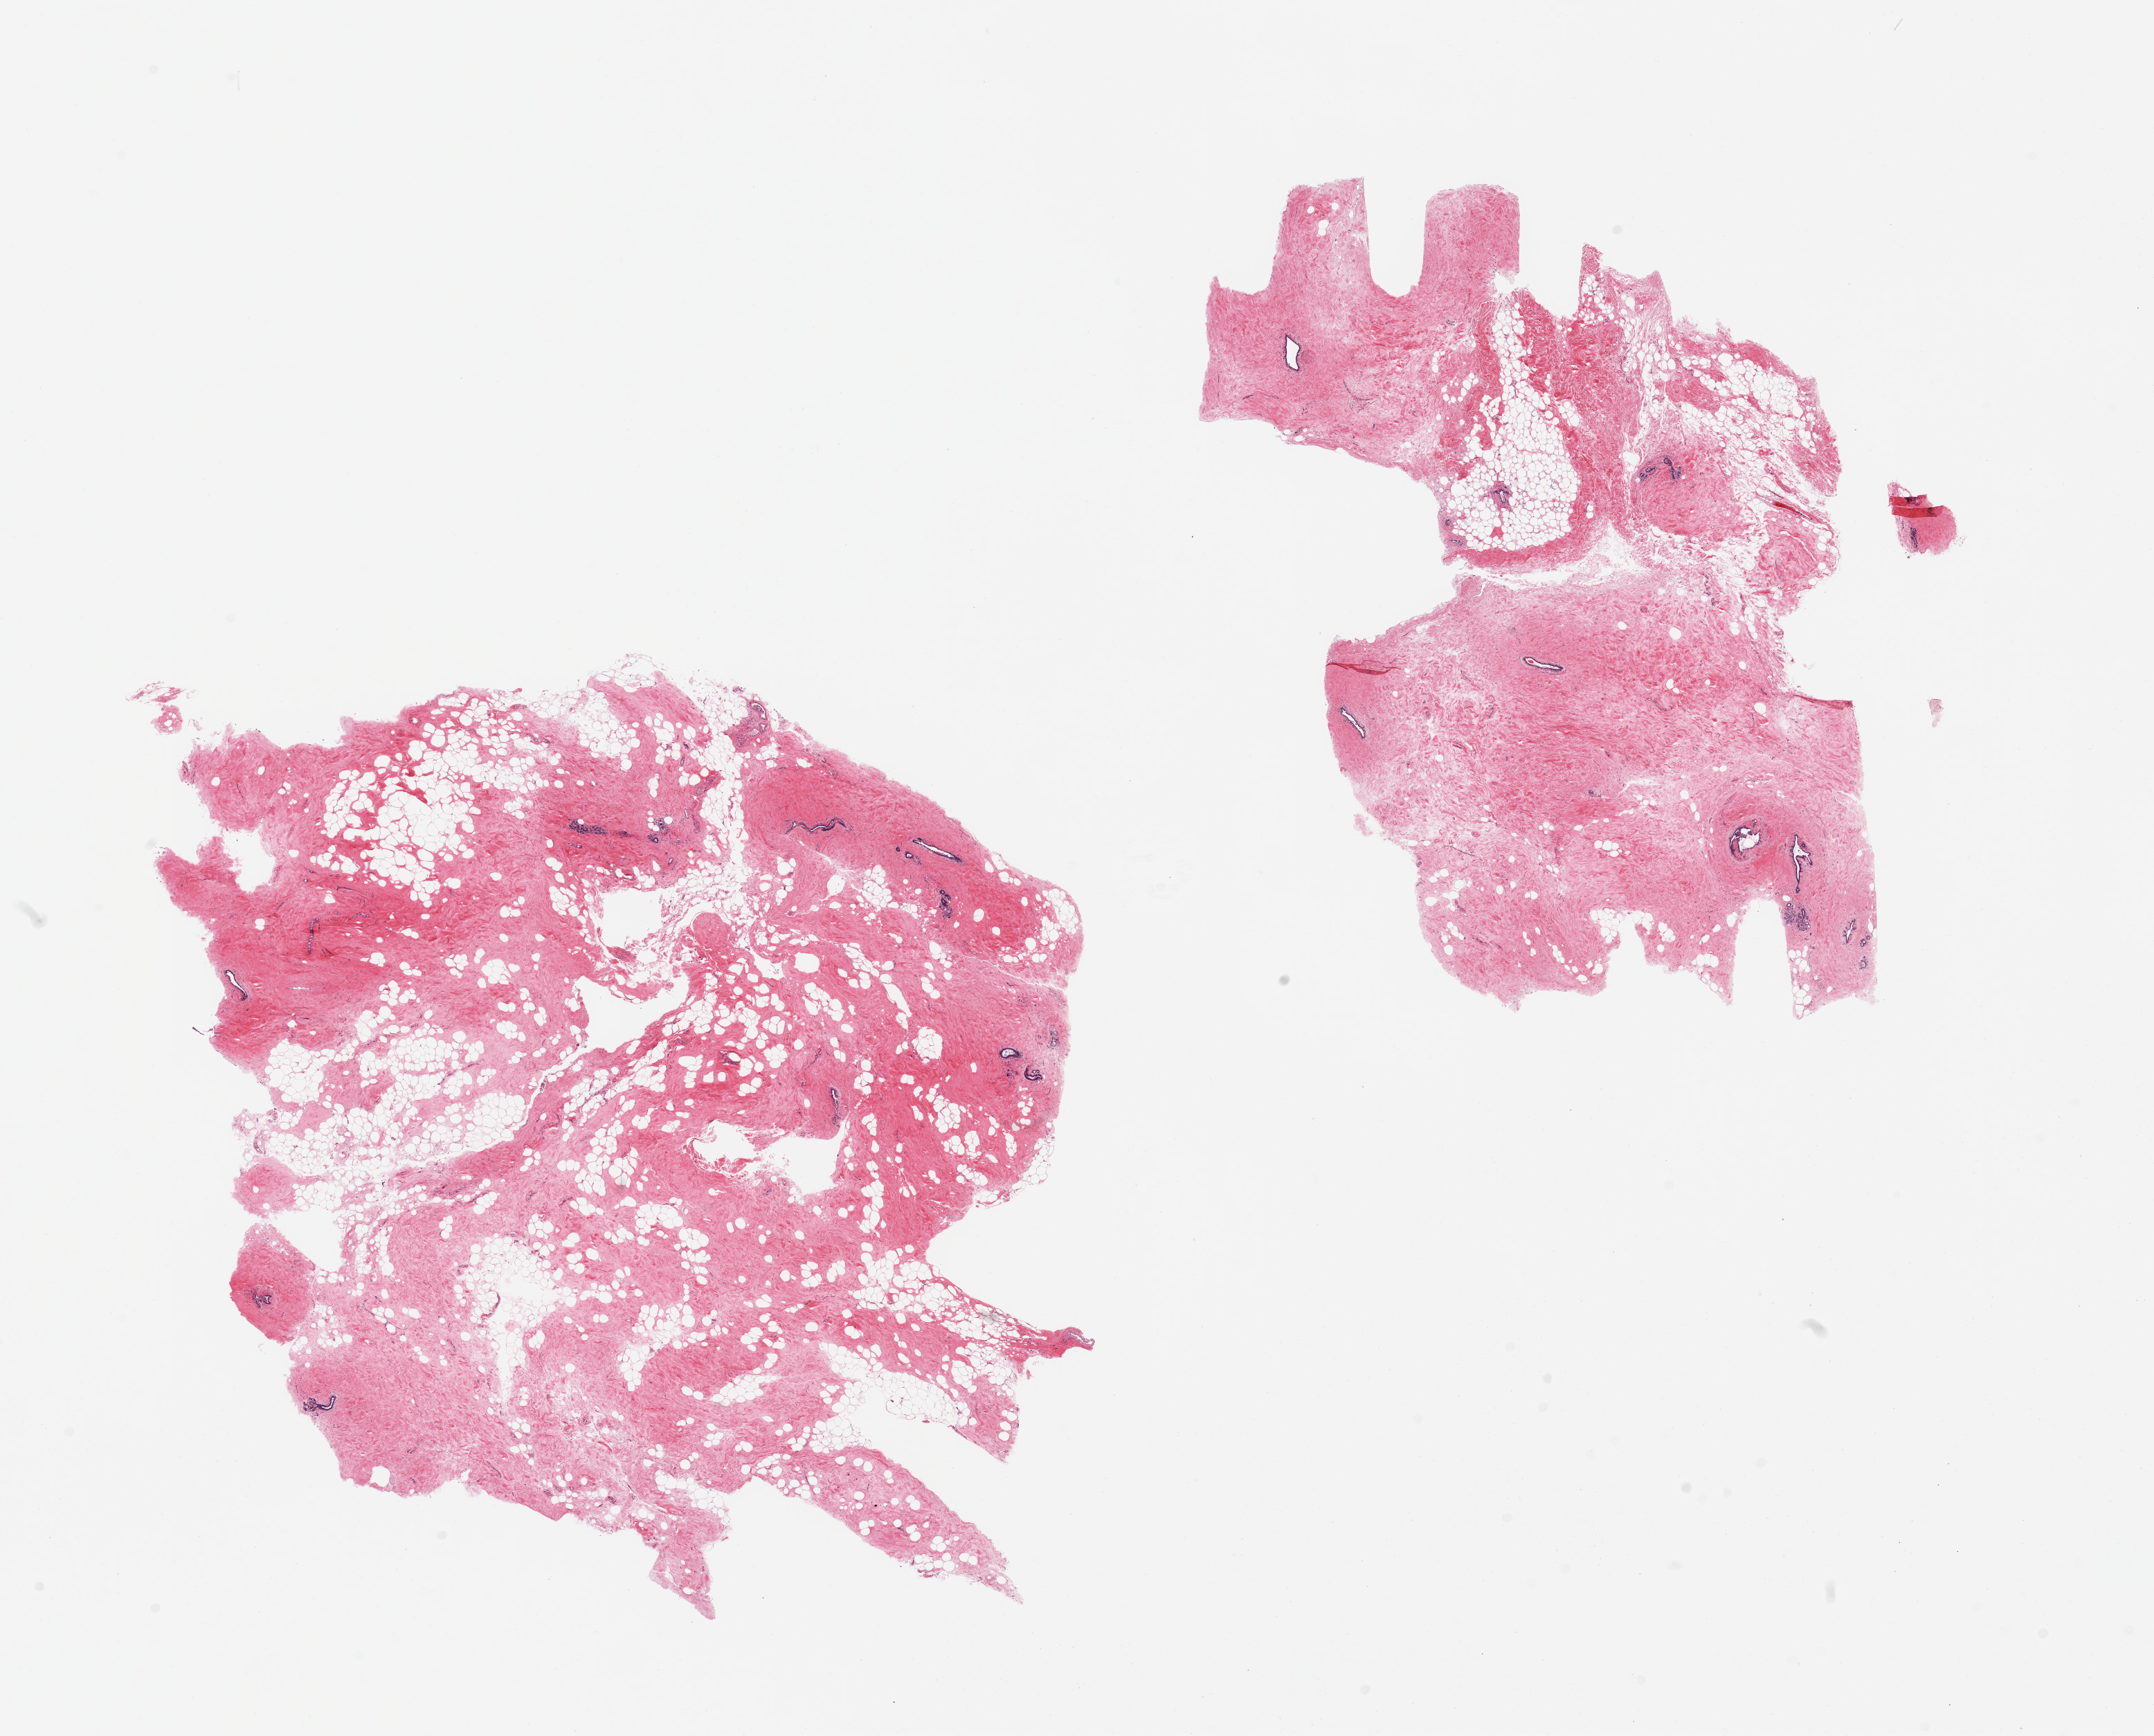
Whole-slide image, H&E stain, shown as a low-resolution overview of the whole scanned area (about 24.6 x 19.8 mm, slide scanned at 20x); PAXgene-fixed, paraffin-embedded tissue; sampled site (target tissue): breast; tissue donor sample. Female donor.
Reviewer comment on this tissue sample: 2 pieces; fat and fibrocollagenous stroma with benign ductal/lobular elements.